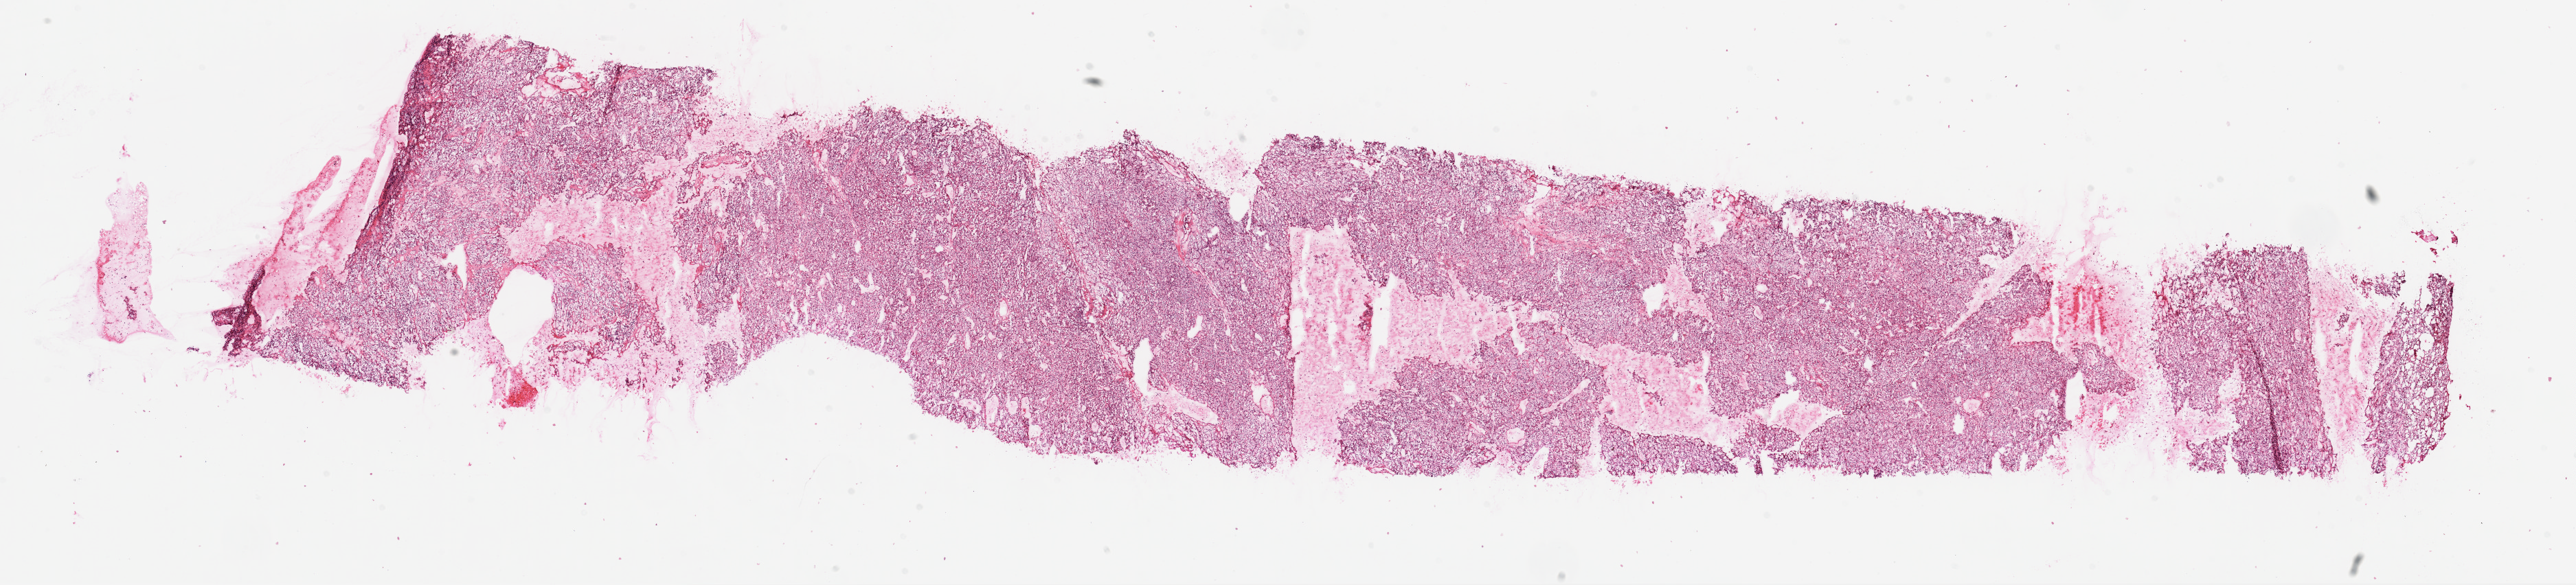
Digitized Hematoxylin and eosin (H&E) stained tissue section (whole slide) — a low-resolution overview of the entire scanned area, about 30.1 x 6.8 mm (slide scanned at 20x), frozen section from the top of the tissue portion, kidney, primary tumour sample. Patient: female, age at initial diagnosis 58 years. Histologic grade: G2 (moderately differentiated). Composition of this section per pathologist review: tumour cells 85%, tumour nuclei 85%, normal cells 0%, stromal cells 15%, necrosis 0%.
AJCC pathologic stage: III. Laterality: left. TNM: T3a NX M0. Histologic diagnosis: Clear cell adenocarcinoma, NOS.